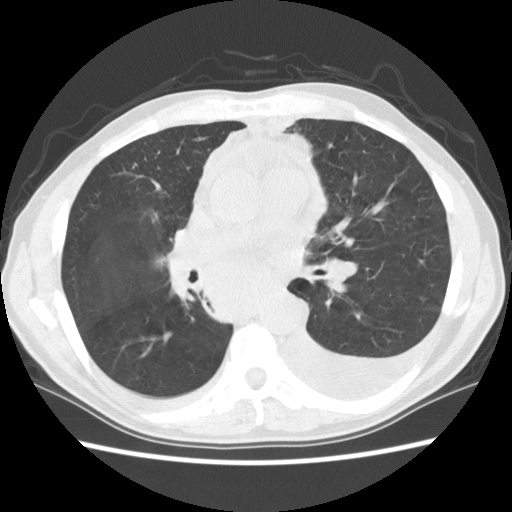
Chest CT (low-dose screening protocol), one axial image; baseline annual screen; lung window (W 1500 / L -600 HU); 2.5 mm slice thickness; standard (soft-tissue) reconstruction kernel (STANDARD); slice 56 of 135 in the series. Male, age 60 years at enrolment.
- Expert reader's lesion annotation, bounding box (x1, y1, x2, y2) in pixels: (175, 240, 302, 332).
- Screening reader's record for this exam: no non-calcified nodule ≥4 mm recorded.
- Official screen result: negative screen, significant abnormalities not suspicious for lung cancer.
- Lung cancer was diagnosed 12 days after this screen: squamous cell carcinoma, NOS, carina, poorly differentiated (G3), stage IV (AJCC 6th edition).